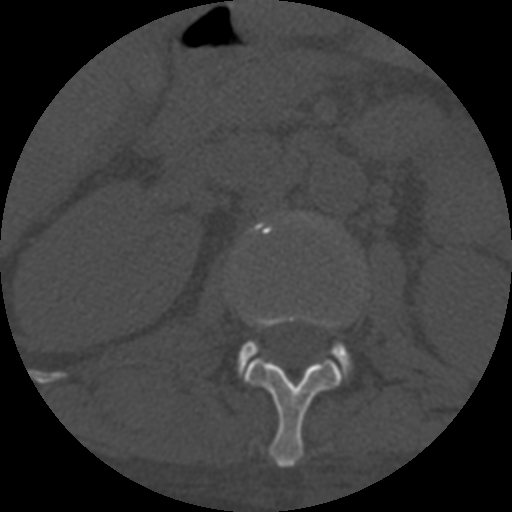
CT including the spine, one axial slice. Position 276 of 708 along the scan axis. 120 kVp. One of 3 acquisitions stored at this slice position. Bone window (W 1800 / L 400 HU). 1.25 mm slice thickness. 512 × 512 image matrix, field of view 160 × 160 mm. Patient age 55 years. Case-level facts recorded for this patient, not image findings: primary cancer: colon; vertebrae with lytic lesions (as recorded): T12, L1, L5.
Annotated regions visible in this slice (semi-automatically segmented with operator editing):
- L1 vertebra: bounding box [x1, y1, x2, y2] px = [242, 309, 344, 467]
- L2 vertebra: [239, 221, 351, 369]